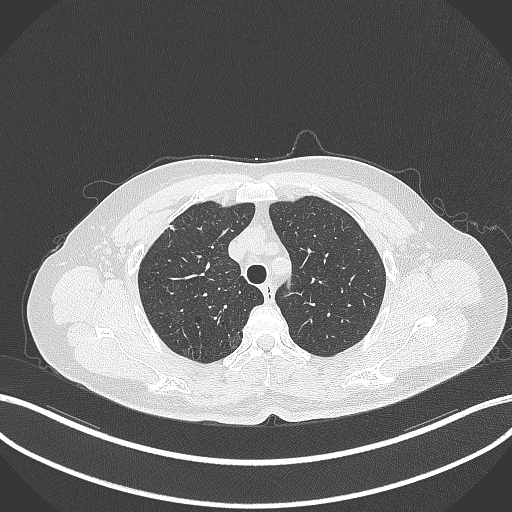
Chest CT, one axial slice. Slice 291 of 353 in the series (ordered by position). Lung window (W 1500 / L -600 HU). 512 × 512 image matrix, field of view 400 × 400 mm. Patient: female, 56 years. From the clinical record (not read from this slice): clinical TNM (as recorded): T1c N0 M0.
Outlined on this slice (rectangle marked by the reading radiologist):
- lung tumour (recorded histology: adenocarcinoma): bounding box (x1, y1, x2, y2) in pixels: (167, 220, 179, 235)